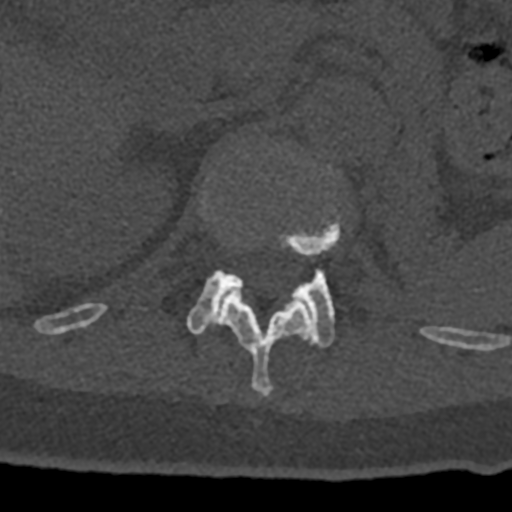
CT including the spine, one axial slice; slice 464 of 797 in the series (ordered by position); reconstruction kernel Br40s/3; 120 kVp; bone window (W 1800 / L 400 HU); 0.5 mm slice thickness; 512 × 512 image matrix, field of view 160 × 160 mm. Male patient, age 74 years. From the clinical record (not read from this slice): primary cancer: renal.
Outlined on this slice (semi-automatically segmented with operator editing):
- L1 vertebra: bounding box [x1, y1, x2, y2] px = [187, 168, 341, 348]
- T12 vertebra: [70, 196, 432, 396]